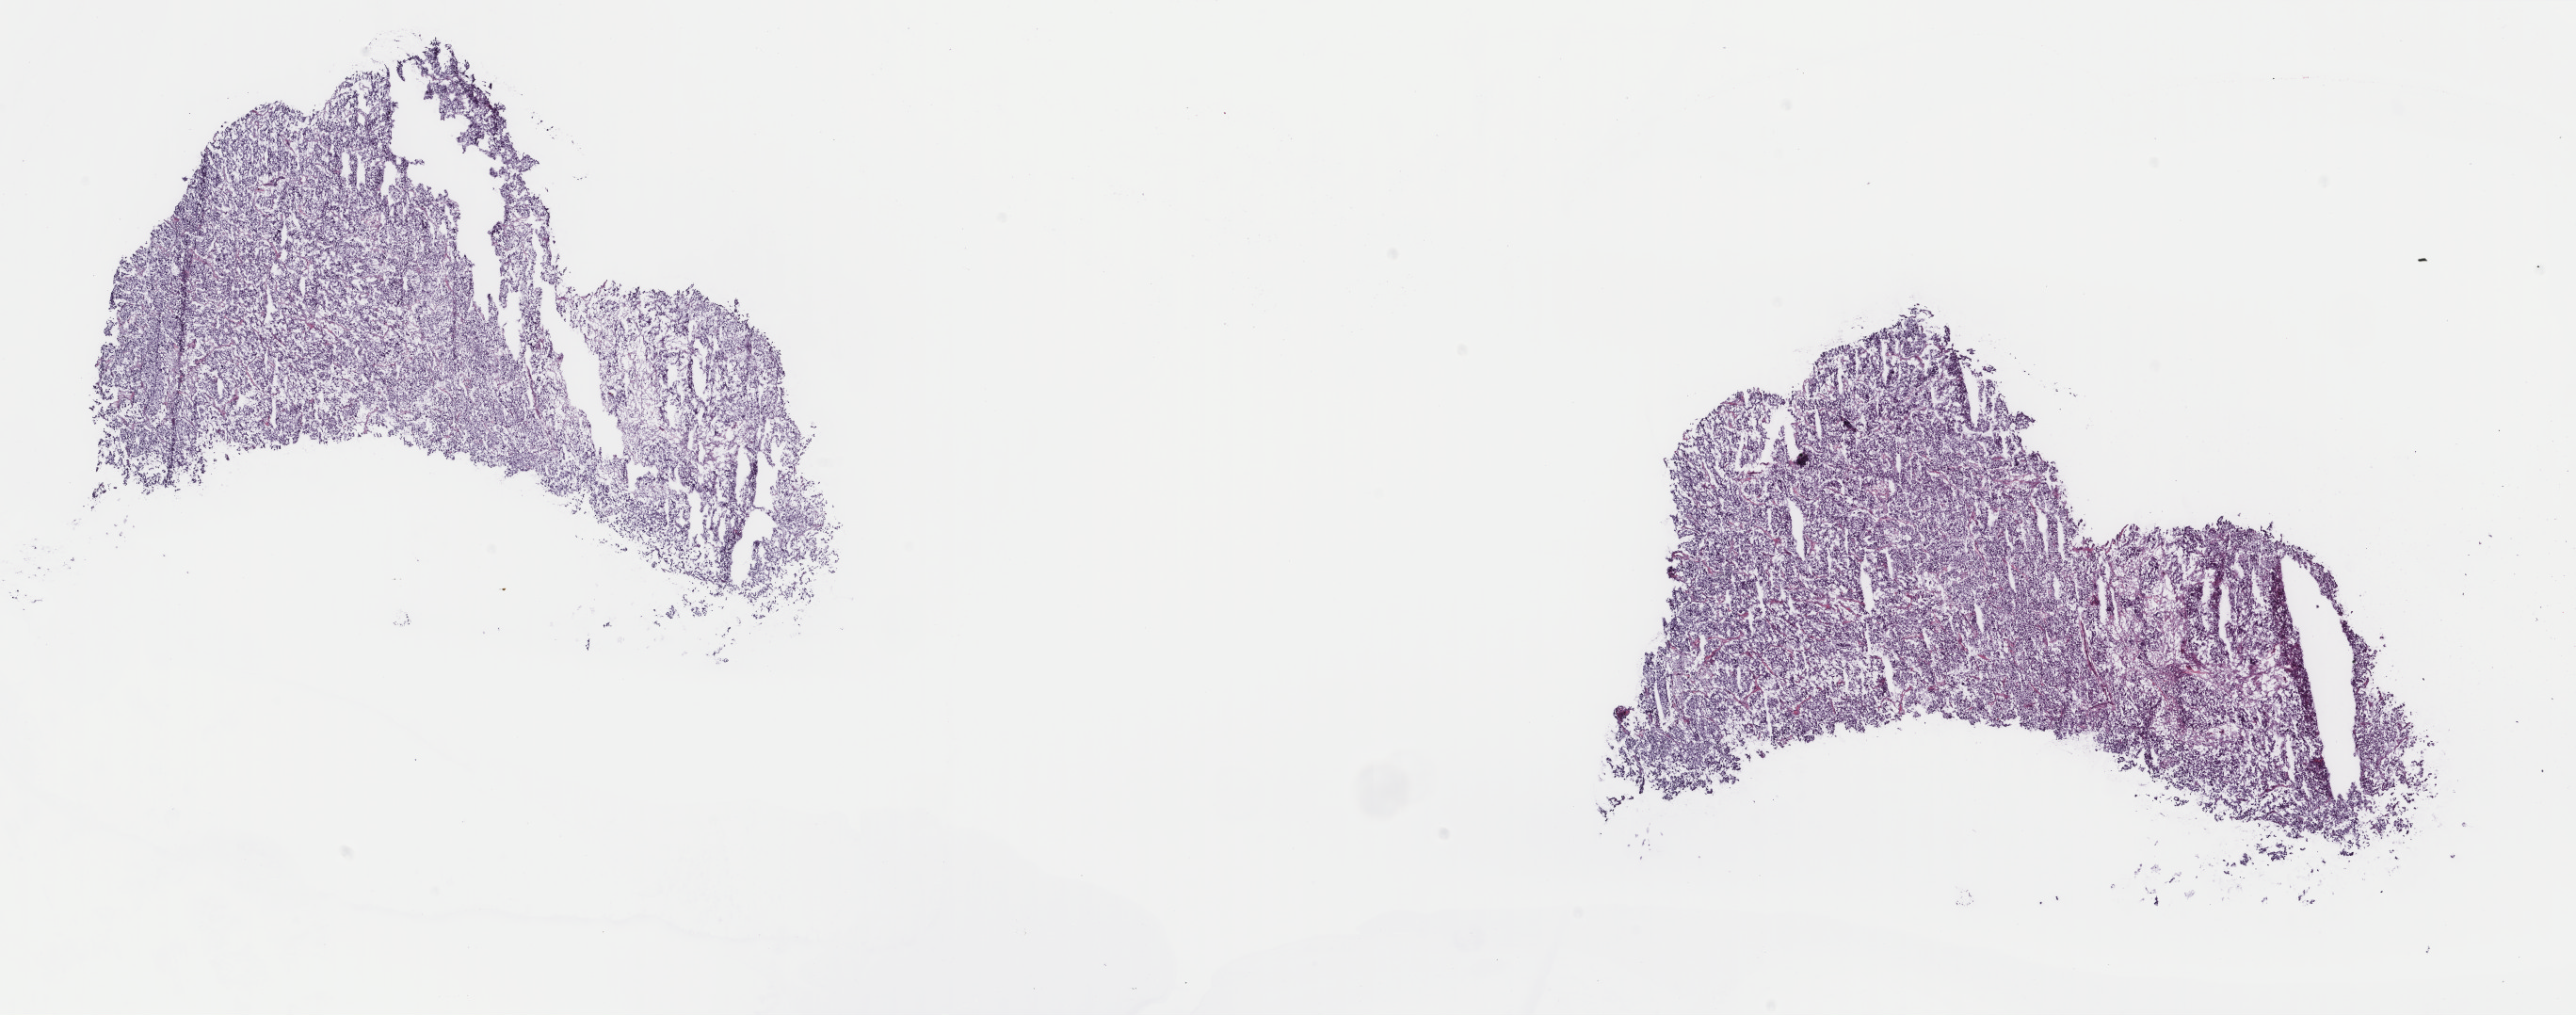
H&E whole-slide image, shown as a low-resolution overview of the whole scanned area (about 21.7 x 8.6 mm, from a 40x scan), frozen section, sample: primary tumour, adrenal gland. Female patient; age at initial diagnosis 35 years. Composition of this section per pathologist review: tumour cells 100%, tumour nuclei 80%, normal cells 0%, stromal cells 0%, necrosis 0%. Inflammatory infiltration, as recorded: lymphocyte infiltration 1%, monocyte infiltration 0%, neutrophil infiltration 0%.
Laterality: right. Diagnosis: Pheochromocytoma, NOS.